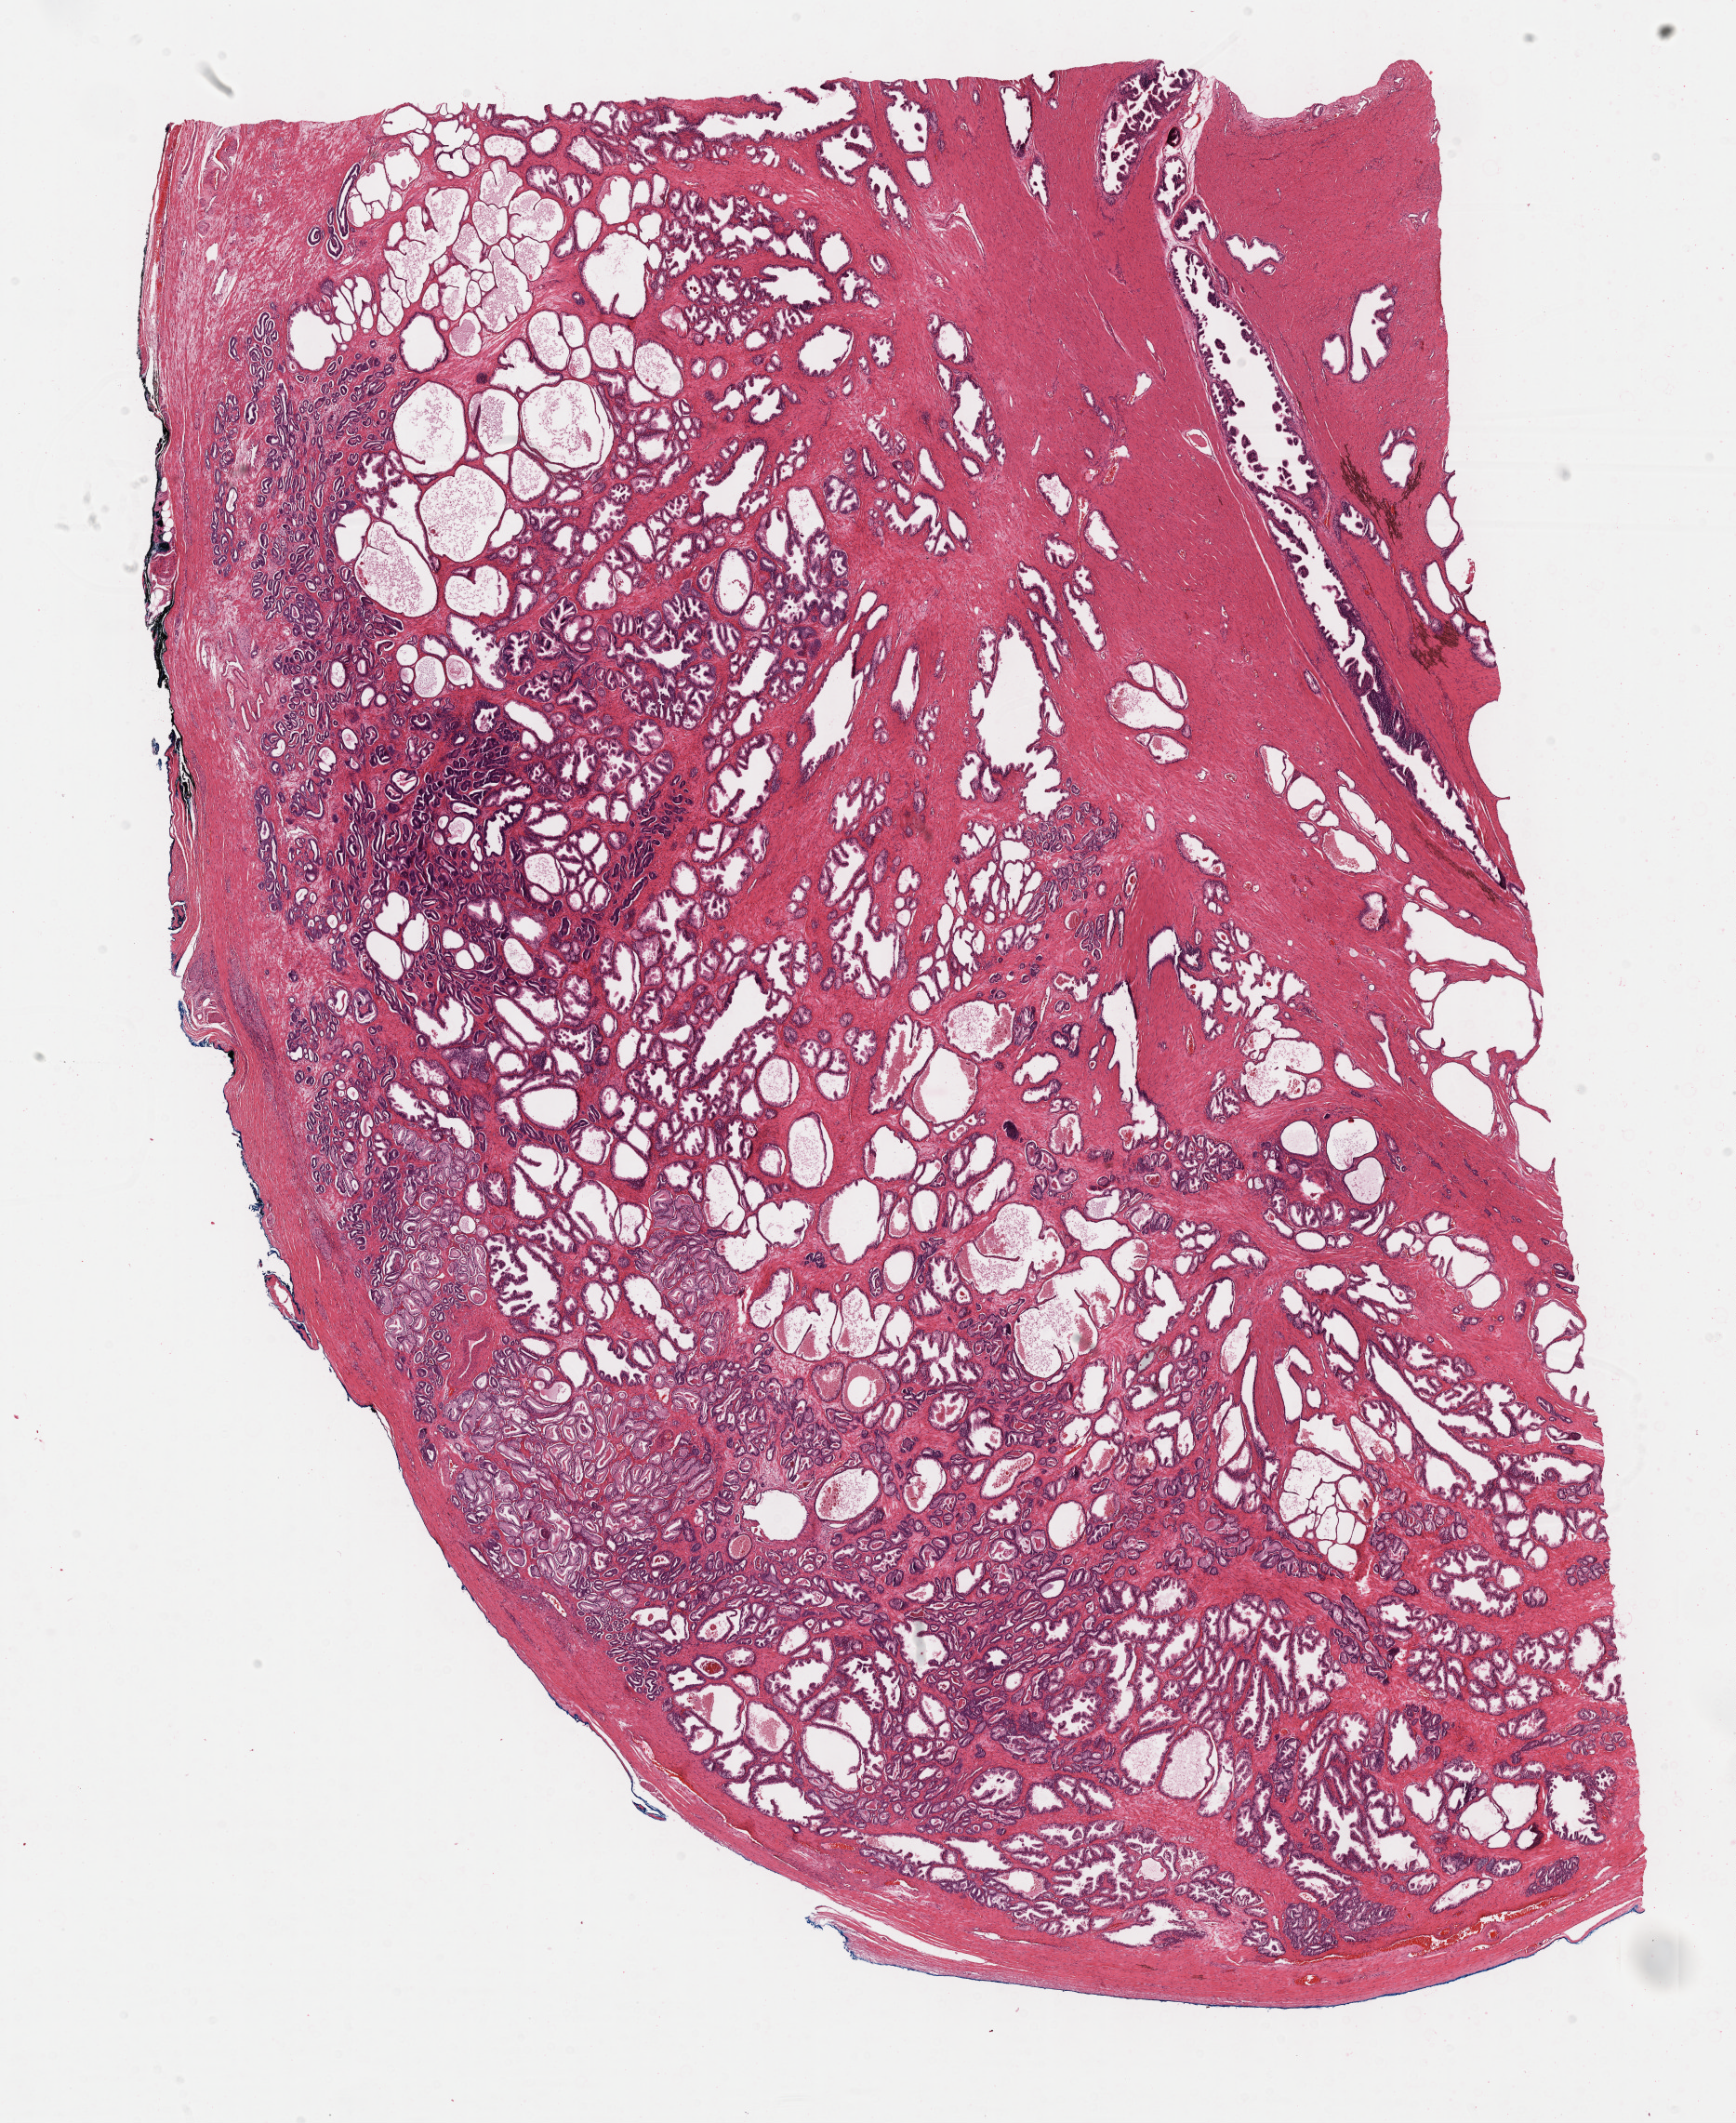
H&E whole-slide image — whole scanned area (about 15.1 x 18.5 mm) shown as a low-resolution overview; formalin-fixed paraffin-embedded (FFPE) diagnostic section; prostate, primary tumour sample. Patient: male, age at initial diagnosis 52 years. Gleason score: 6 (3+3).
Pathologic diagnosis: Adenocarcinoma, NOS (prostate gland).